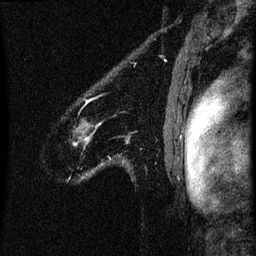
Breast MRI (dynamic contrast-enhanced), one sagittal slice. Position 56 of 60 along the scan axis. Dynamic contrast-enhanced series, image 2 of 3 at this slice position (ordered by acquisition). 1.5 T. TE 4.2 ms, TR 8 ms. 256 × 256 image matrix. Patient: female, 61 years.
Structures marked on this image (semi-automatically segmented with operator editing):
- analysis volume of interest (the breast-tissue region the enhancement analysis was run in; not a lesion): bounding box [x1, y1, x2, y2] px = [73, 100, 102, 177]
- tumour enhancement mask (voxels above the 70 % enhancement threshold inside the analysis volume of interest): [86, 100, 89, 103]